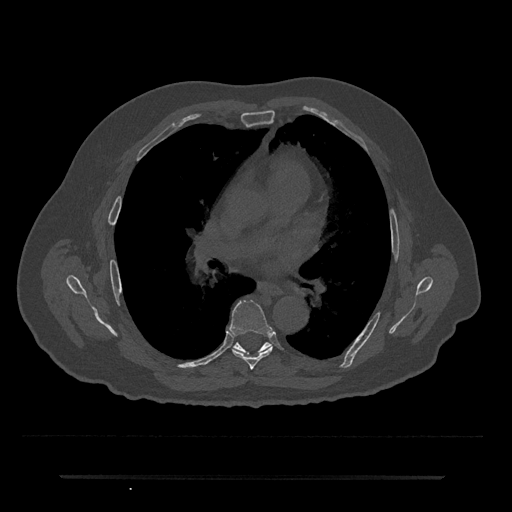
CT including the spine, one axial slice. Slice 420 of 797 in the series (ordered by position). Reconstruction kernel Br40s/3. Bone window (W 1800 / L 400 HU). 0.5 mm slice thickness. 512 × 512 image matrix, field of view 437 × 437 mm. Male patient, age 69 years. From the clinical record (not read from this slice): primary cancer: prostate.
Outlined on this slice (semi-automatic segmentation, software-assisted and operator-edited):
- T6 vertebra: box from (x=229, y=299) to (x=275, y=370) px
- T7 vertebra: (x=233, y=343)–(x=271, y=351)